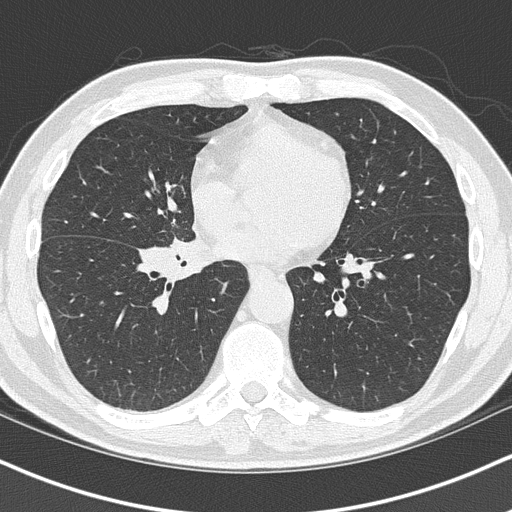
Axial slice from a low-dose chest CT screening exam; first (baseline) screen; lung window (W 1500 / L -600 HU); 2 mm slice thickness; lung (sharp) reconstruction kernel (B50f); slice 55 of 151 in the series. Male, age 55 years at enrolment. Current smoker at enrolment.
Expert-annotated lung lesion, bounding box (x1, y1, x2, y2) in pixels: (134, 226, 239, 305). The exam's reader record, not a measurement of the box and not confirmed to be the same lesion: non-calcified nodule or mass ≥4 mm, right lower lobe, 6 × 5 mm, spiculated (stellate) margins, soft tissue attenuation. Official screen result: positive, change unspecified: nodule(s) >= 4 mm or enlarging nodule(s), mass(es), or other non-specific abnormalities suspicious for lung cancer.